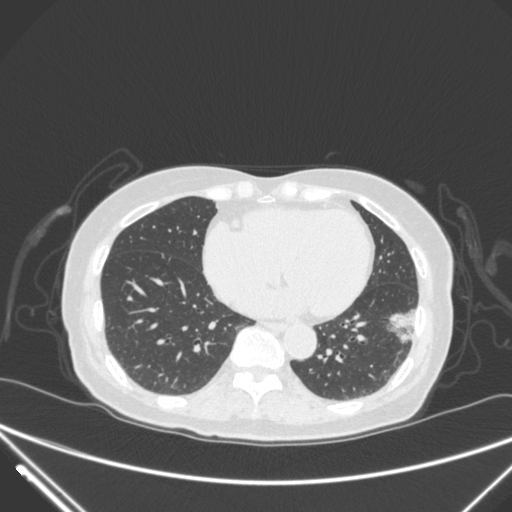
Chest CT, one axial slice. 120 kVp. Lung window (W 1500 / L -600 HU). 512 × 512 image matrix, field of view 377 × 377 mm. Patient: female, 82 years. Case-level facts recorded for this patient, not image findings: clinical TNM (as recorded): T1c N0 M0; histopathological grade: G2.
Annotated regions visible in this slice (rectangle marked by the reading radiologist):
- lung tumour (recorded histology: adenocarcinoma): bounding box (x1, y1, x2, y2) in pixels: (380, 301, 425, 354)